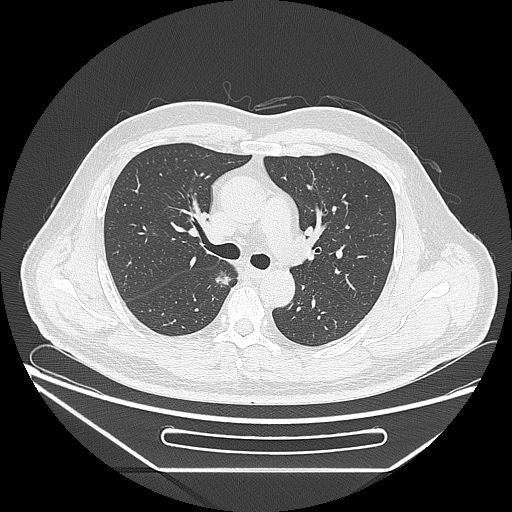
Chest CT, one axial slice; slice 162 of 271 in the series (ordered by position); reconstruction kernel LUNG; 120 kVp; lung window (W 1500 / L -600 HU); 1.25 mm slice thickness; 512 × 512 image matrix, field of view 414 × 414 mm. Male patient, age 49 years. Case-level facts recorded for this patient, not image findings: clinical TNM (as recorded): T1b N0 M0; histopathological grade: G2.
Outlined on this slice (rectangle marked by the reading radiologist):
- lung tumour (recorded histology: adenocarcinoma): bounding box (x1, y1, x2, y2) in pixels: (210, 268, 236, 292)